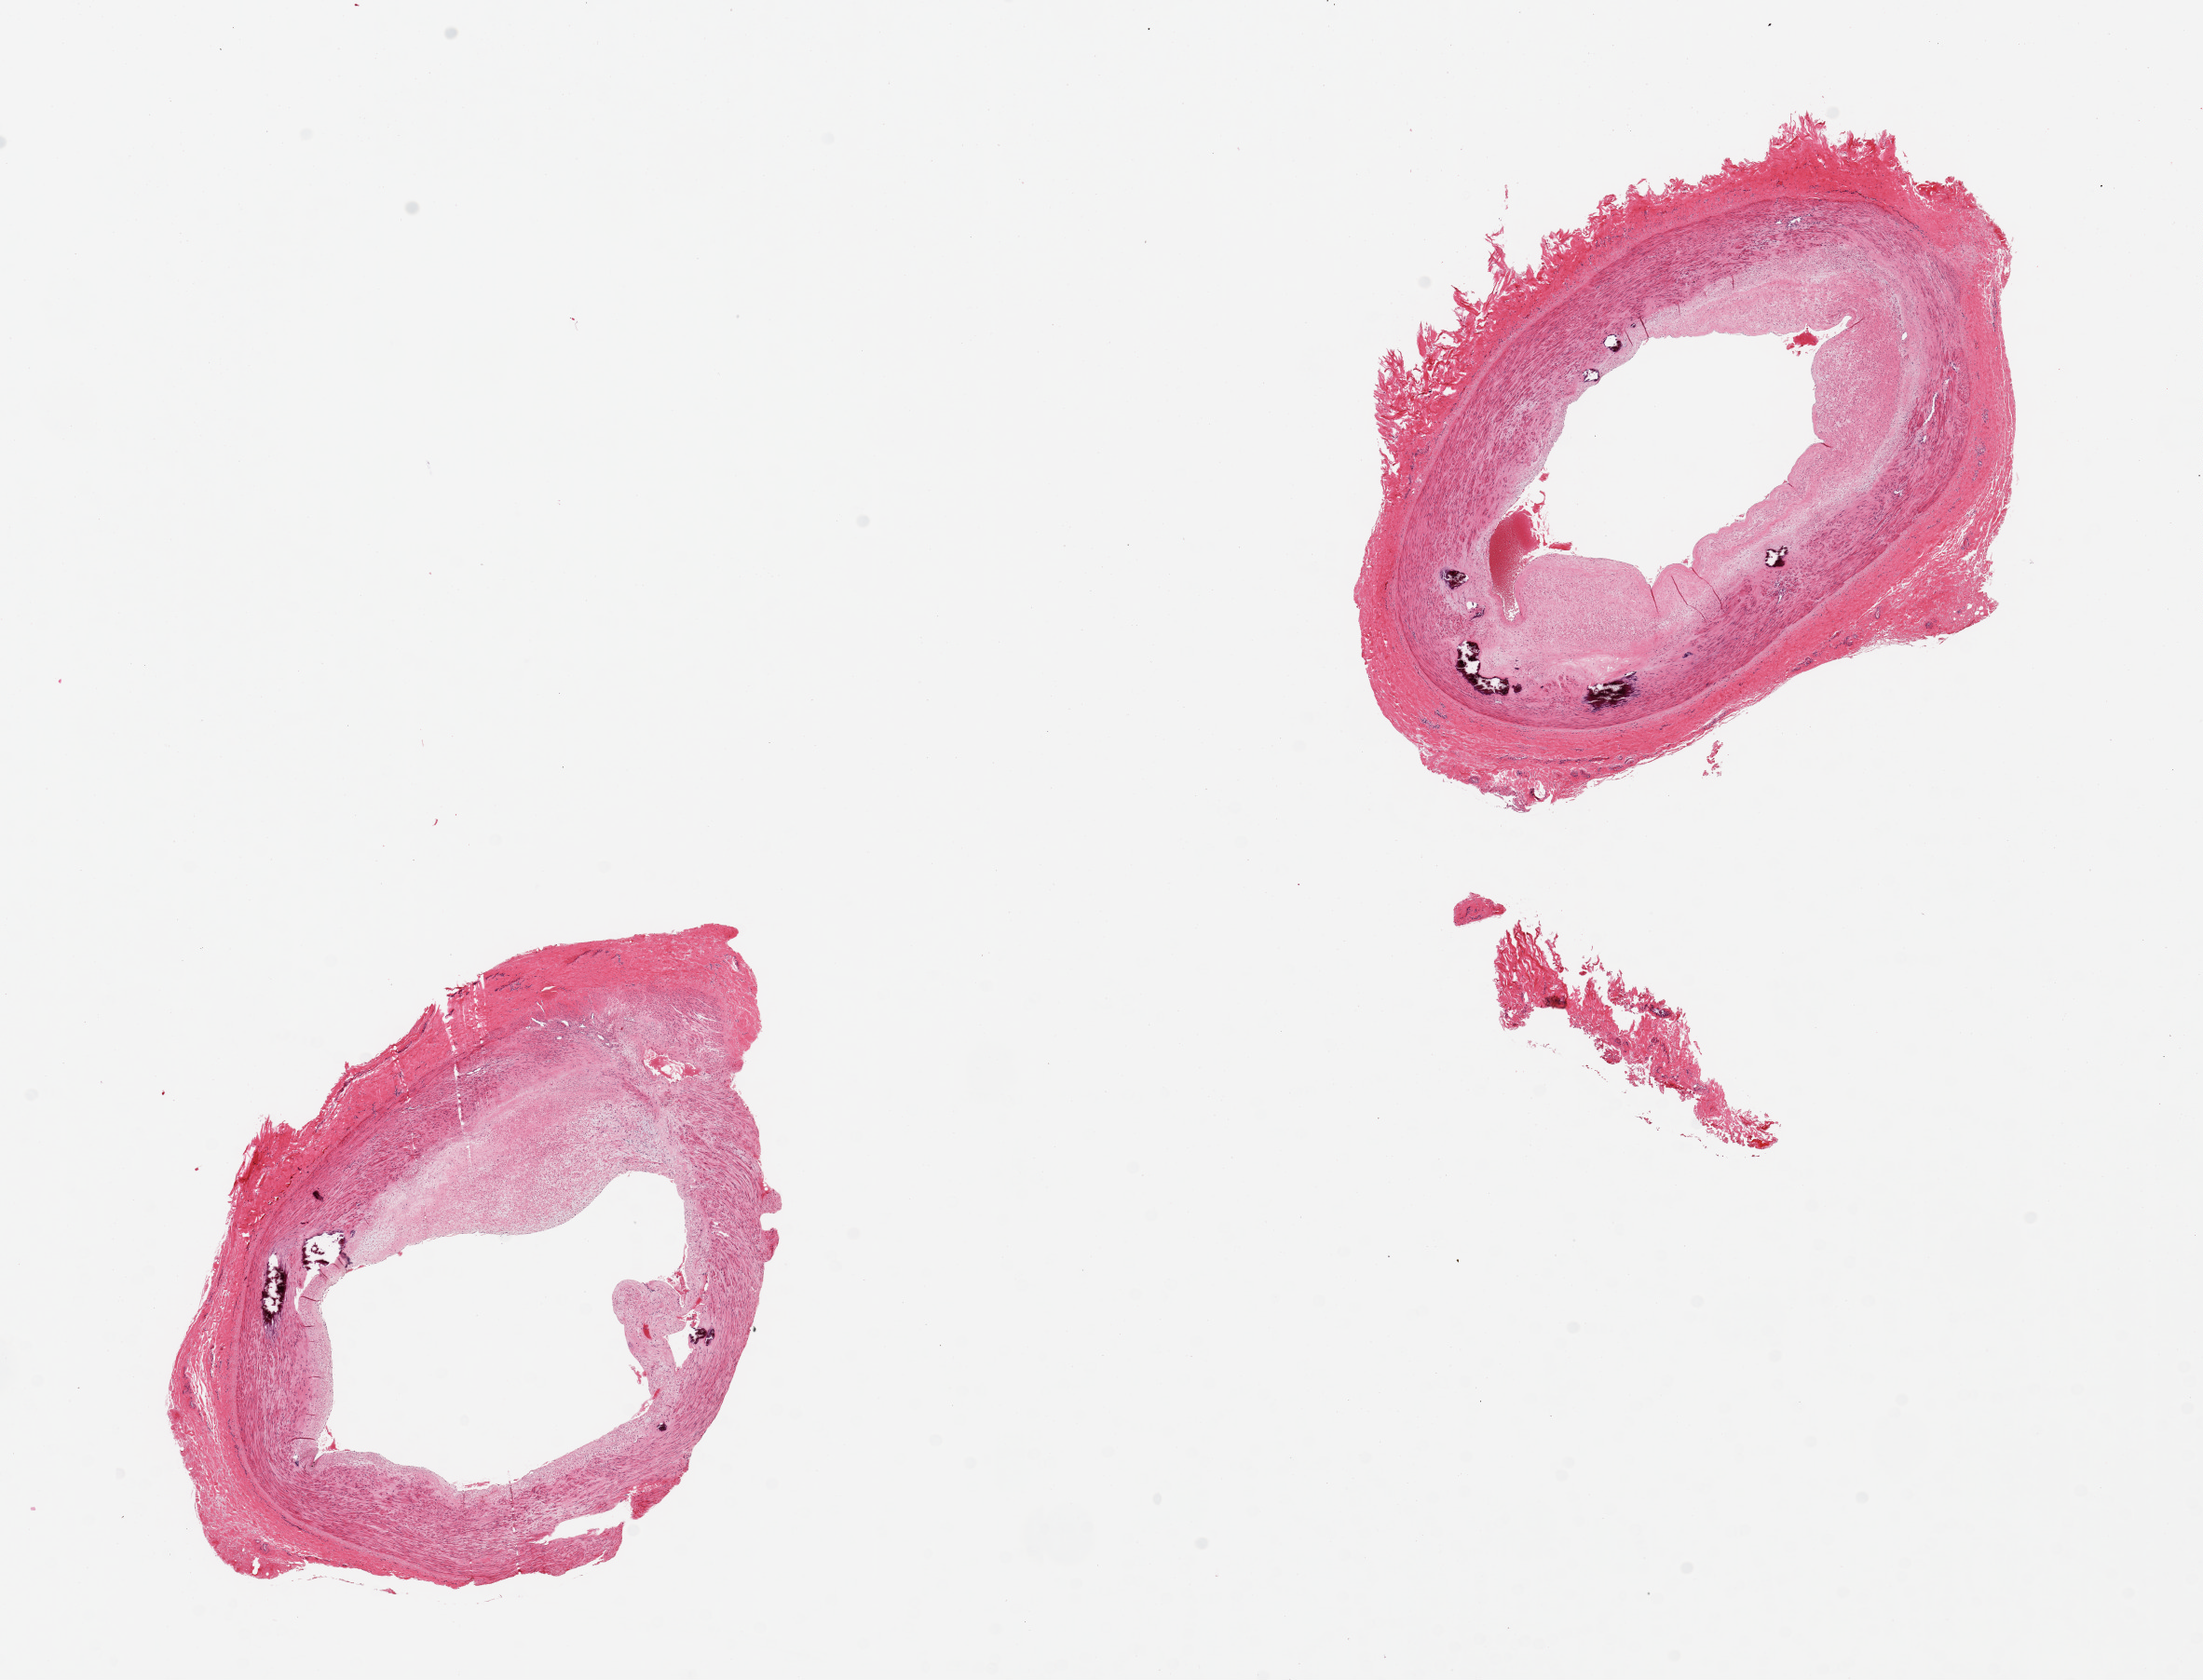
Whole-slide image, hematoxylin and eosin (H&E) stain, brightfield — a low-resolution overview of the entire scanned area, about 18.7 x 14.3 mm (slide scanned at 20x); PAXgene-fixed, paraffin-embedded tissue; target tissue: tibial artery; donor tissue sample. Male donor.
Pathologist's review note for this sample: 2 pieces, not nerve as originally labeled; well trimmed artery with medial calcific sclerosis.